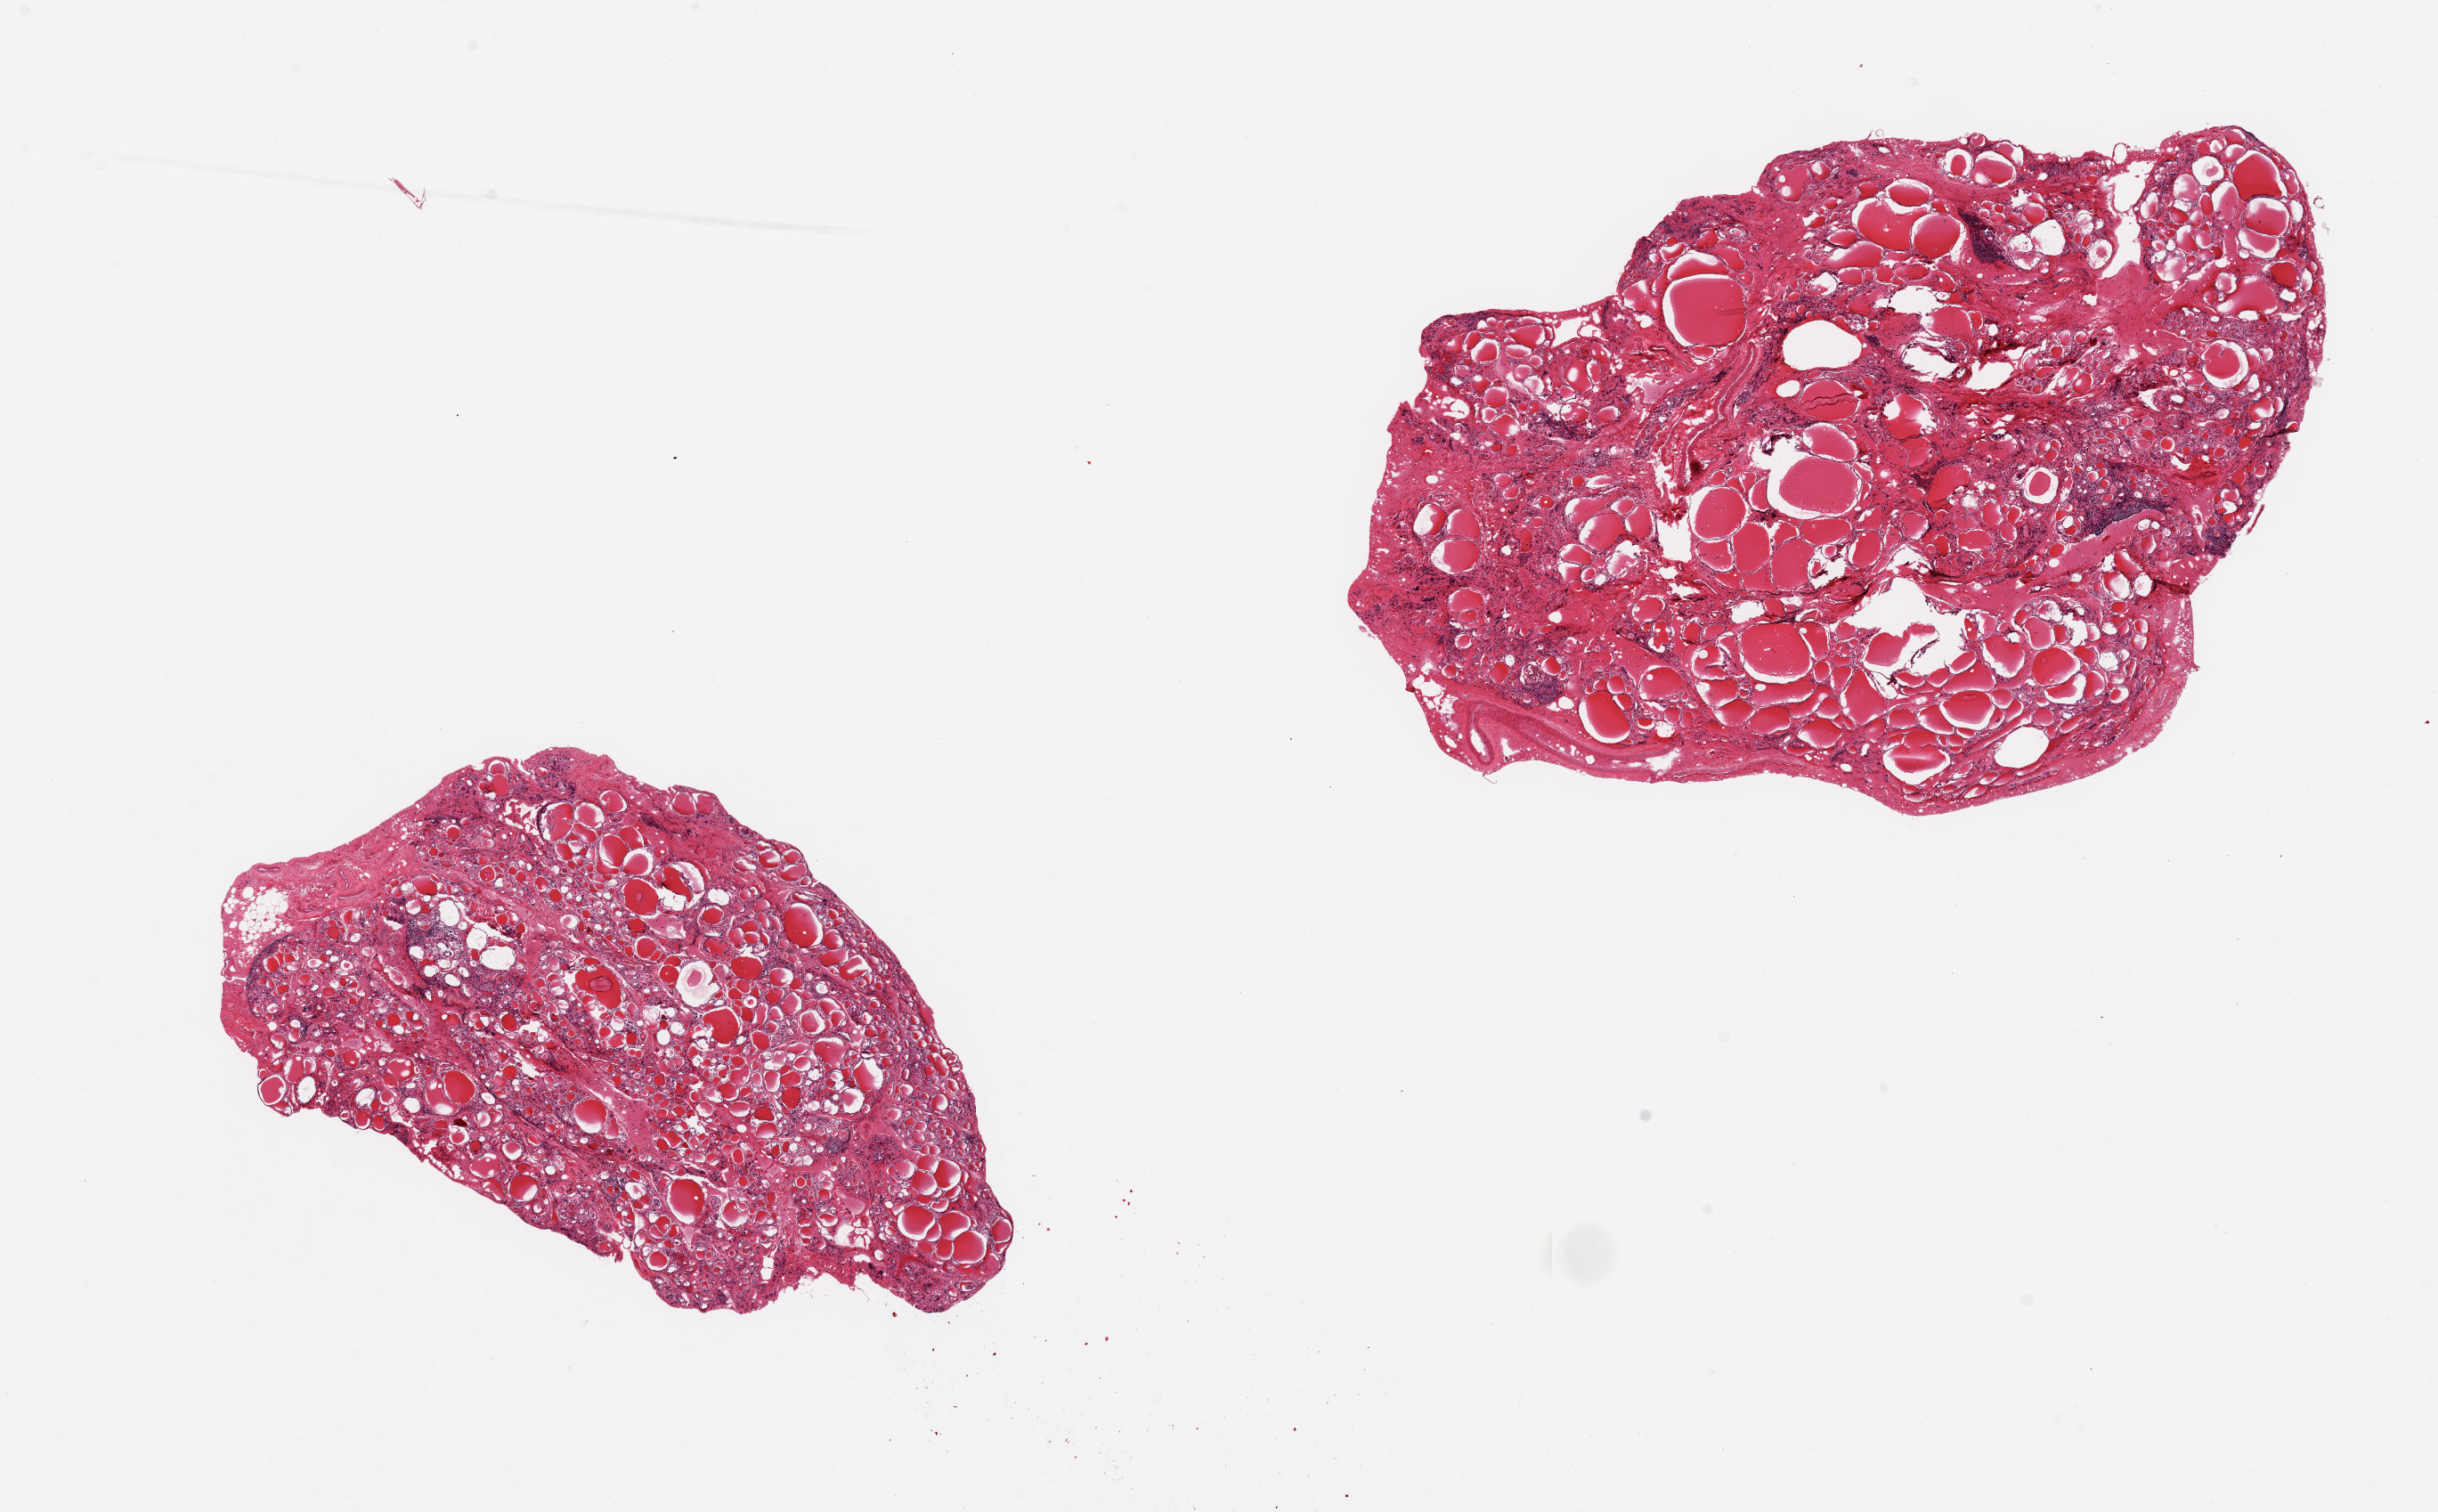
Whole-slide image, H&E stain, a low-resolution overview of the entire scanned area, about 21.7 x 13.4 mm (slide scanned at 20x); PAXgene-fixed, paraffin-embedded tissue; section of thyroid (target tissue); donor tissue sample. Female donor.
- review note (as recorded): 2 pieces, some fibrosis and nodularity with degenerative change and focal chronic inflammation